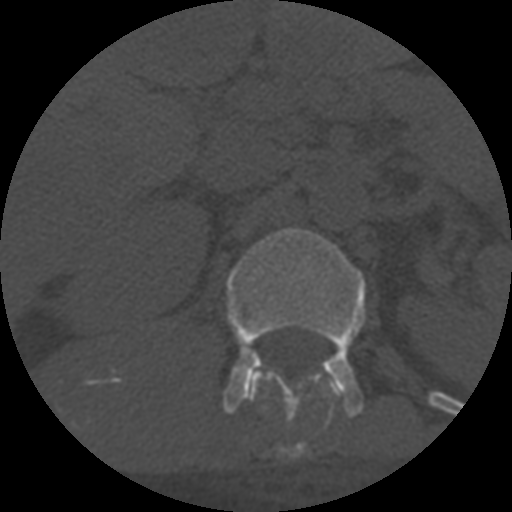
CT including the spine, one axial slice; position 297 of 708 along the scan axis; reconstruction kernel STANDARD; 120 kVp; one of 3 acquisitions stored at this slice position; bone window (W 1800 / L 400 HU); 1.25 mm slice thickness; 512 × 512 image matrix, field of view 160 × 160 mm. Patient age 55 years. Case-level facts recorded for this patient, not image findings: primary cancer: colon; vertebrae with lytic lesions (as recorded): T12, L1, L5.
Structures marked on this image (semi-automatically segmented with operator editing):
- L1 vertebra: bounding box [x1, y1, x2, y2] px = [222, 228, 366, 418]
- T12 vertebra: [248, 371, 332, 458]